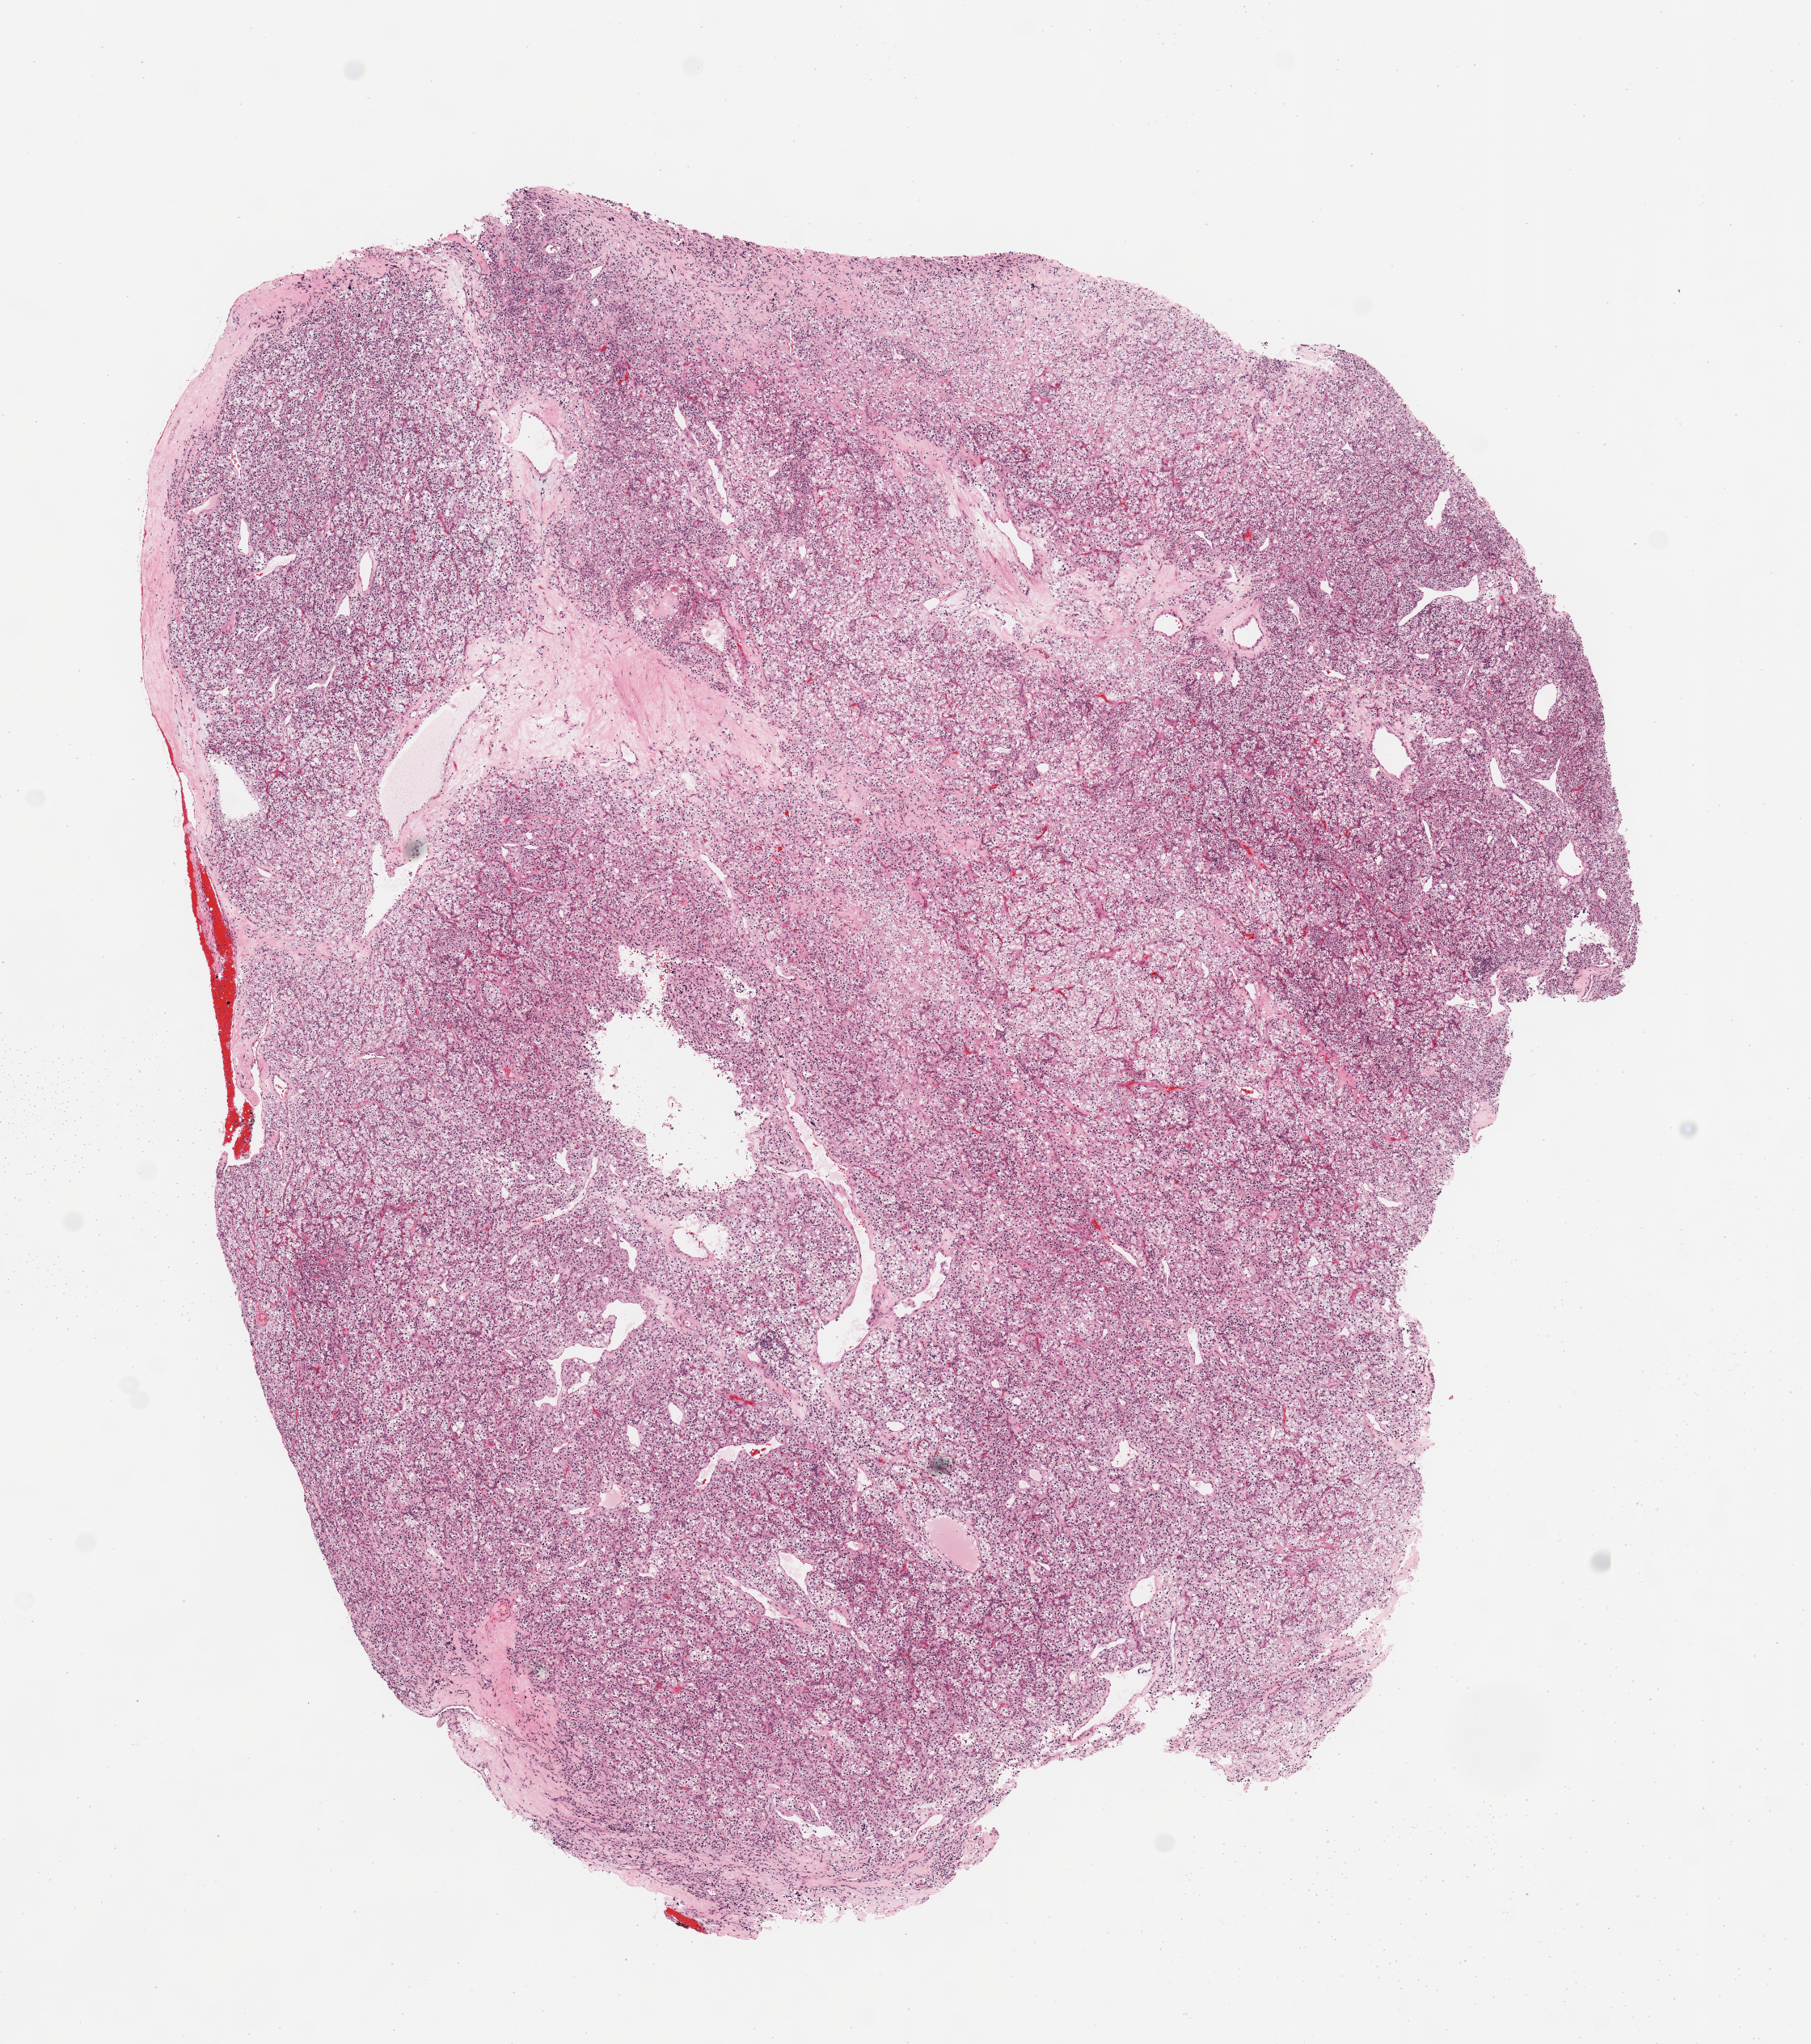
H&E-stained whole-slide image — low-resolution overview of the scanned area, about 8.9 x 10.0 mm (acquisition: 20x scan), kidney, tumour tissue. 66-year-old male patient. Histologic grade: G4 (undifferentiated).
- primary tumour site (as recorded): lower pole
- AJCC pathologic stage: IV
- diagnosis: Renal cell carcinoma, NOS